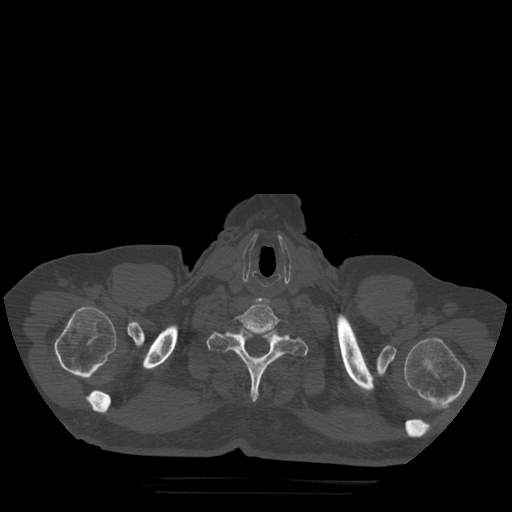
CT including the spine, one axial slice. Position 444 of 522 along the scan axis. Bone window (W 1800 / L 400 HU). 1.25 mm slice thickness. 512 × 512 image matrix. Patient age 72 years. Case-level facts recorded for this patient, not image findings: primary cancer: prostate.
Annotated regions visible in this slice (semi-automatically segmented with operator editing):
- T1 vertebra: bounding box <207,327,308,402> (left, top, right, bottom; pixels)